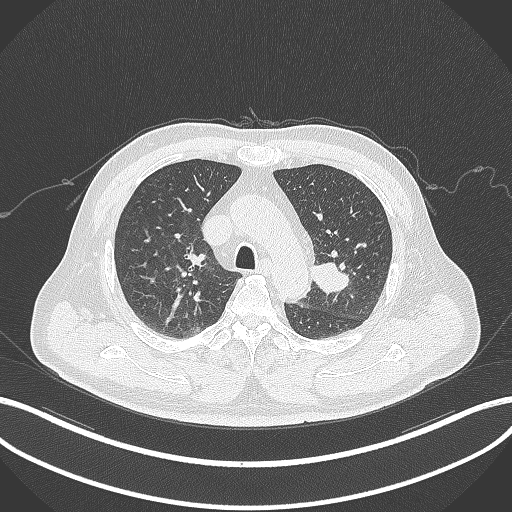
Chest CT, one axial slice; position 217 of 286 along the scan axis; reconstruction kernel B70f; lung window (W 1500 / L -600 HU); 1 mm slice thickness; 512 × 512 image matrix, field of view 400 × 400 mm. Male patient, age 67 years. From the clinical record (not read from this slice): clinical TNM (as recorded): T2a N1 M0; histopathological grade: G3.
Outlined on this slice (rectangle marked by the reading radiologist):
- lung tumour (recorded histology: adenocarcinoma): bounding box <308,256,351,295> (left, top, right, bottom; pixels)